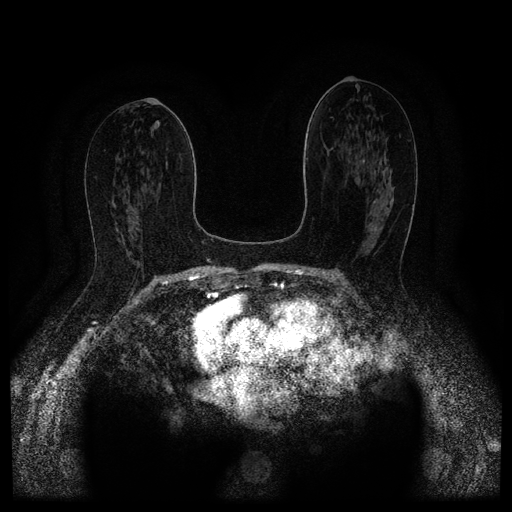
Breast MRI (dynamic contrast-enhanced, multi-phase), one axial slice; slice 56 of 116 in the series (ordered by position); dynamic contrast-enhanced series, time point 2 of 5 at this slice position (early post-contrast); 1.5 T; TE 2.6 ms, TR 5.4 ms; 2 mm slice thickness; 512 × 512 image matrix. Female patient, age 67 years.
Structures marked on this image (semi-automatic segmentation, software-assisted and operator-edited):
- breast lesion (labelled 'tumour' in the annotation; benign lesions carry a separate 'benign' label): bounding box <371,226,382,231> (left, top, right, bottom; pixels)